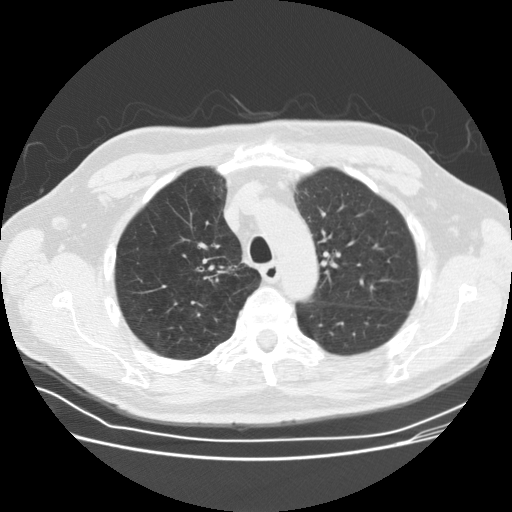
Low-dose screening chest CT, one axial slice. Slice 120 of 164 in the series (ordered by position). Reconstruction kernel STANDARD. 120 kVp. Lung window (W 1500 / L -600 HU). 512 × 512 image matrix.
Structures marked on this image (outlined manually by an expert reader):
- lesion 1 (tumor, upper lobe of right lung): box from (x=228, y=264) to (x=238, y=271) px